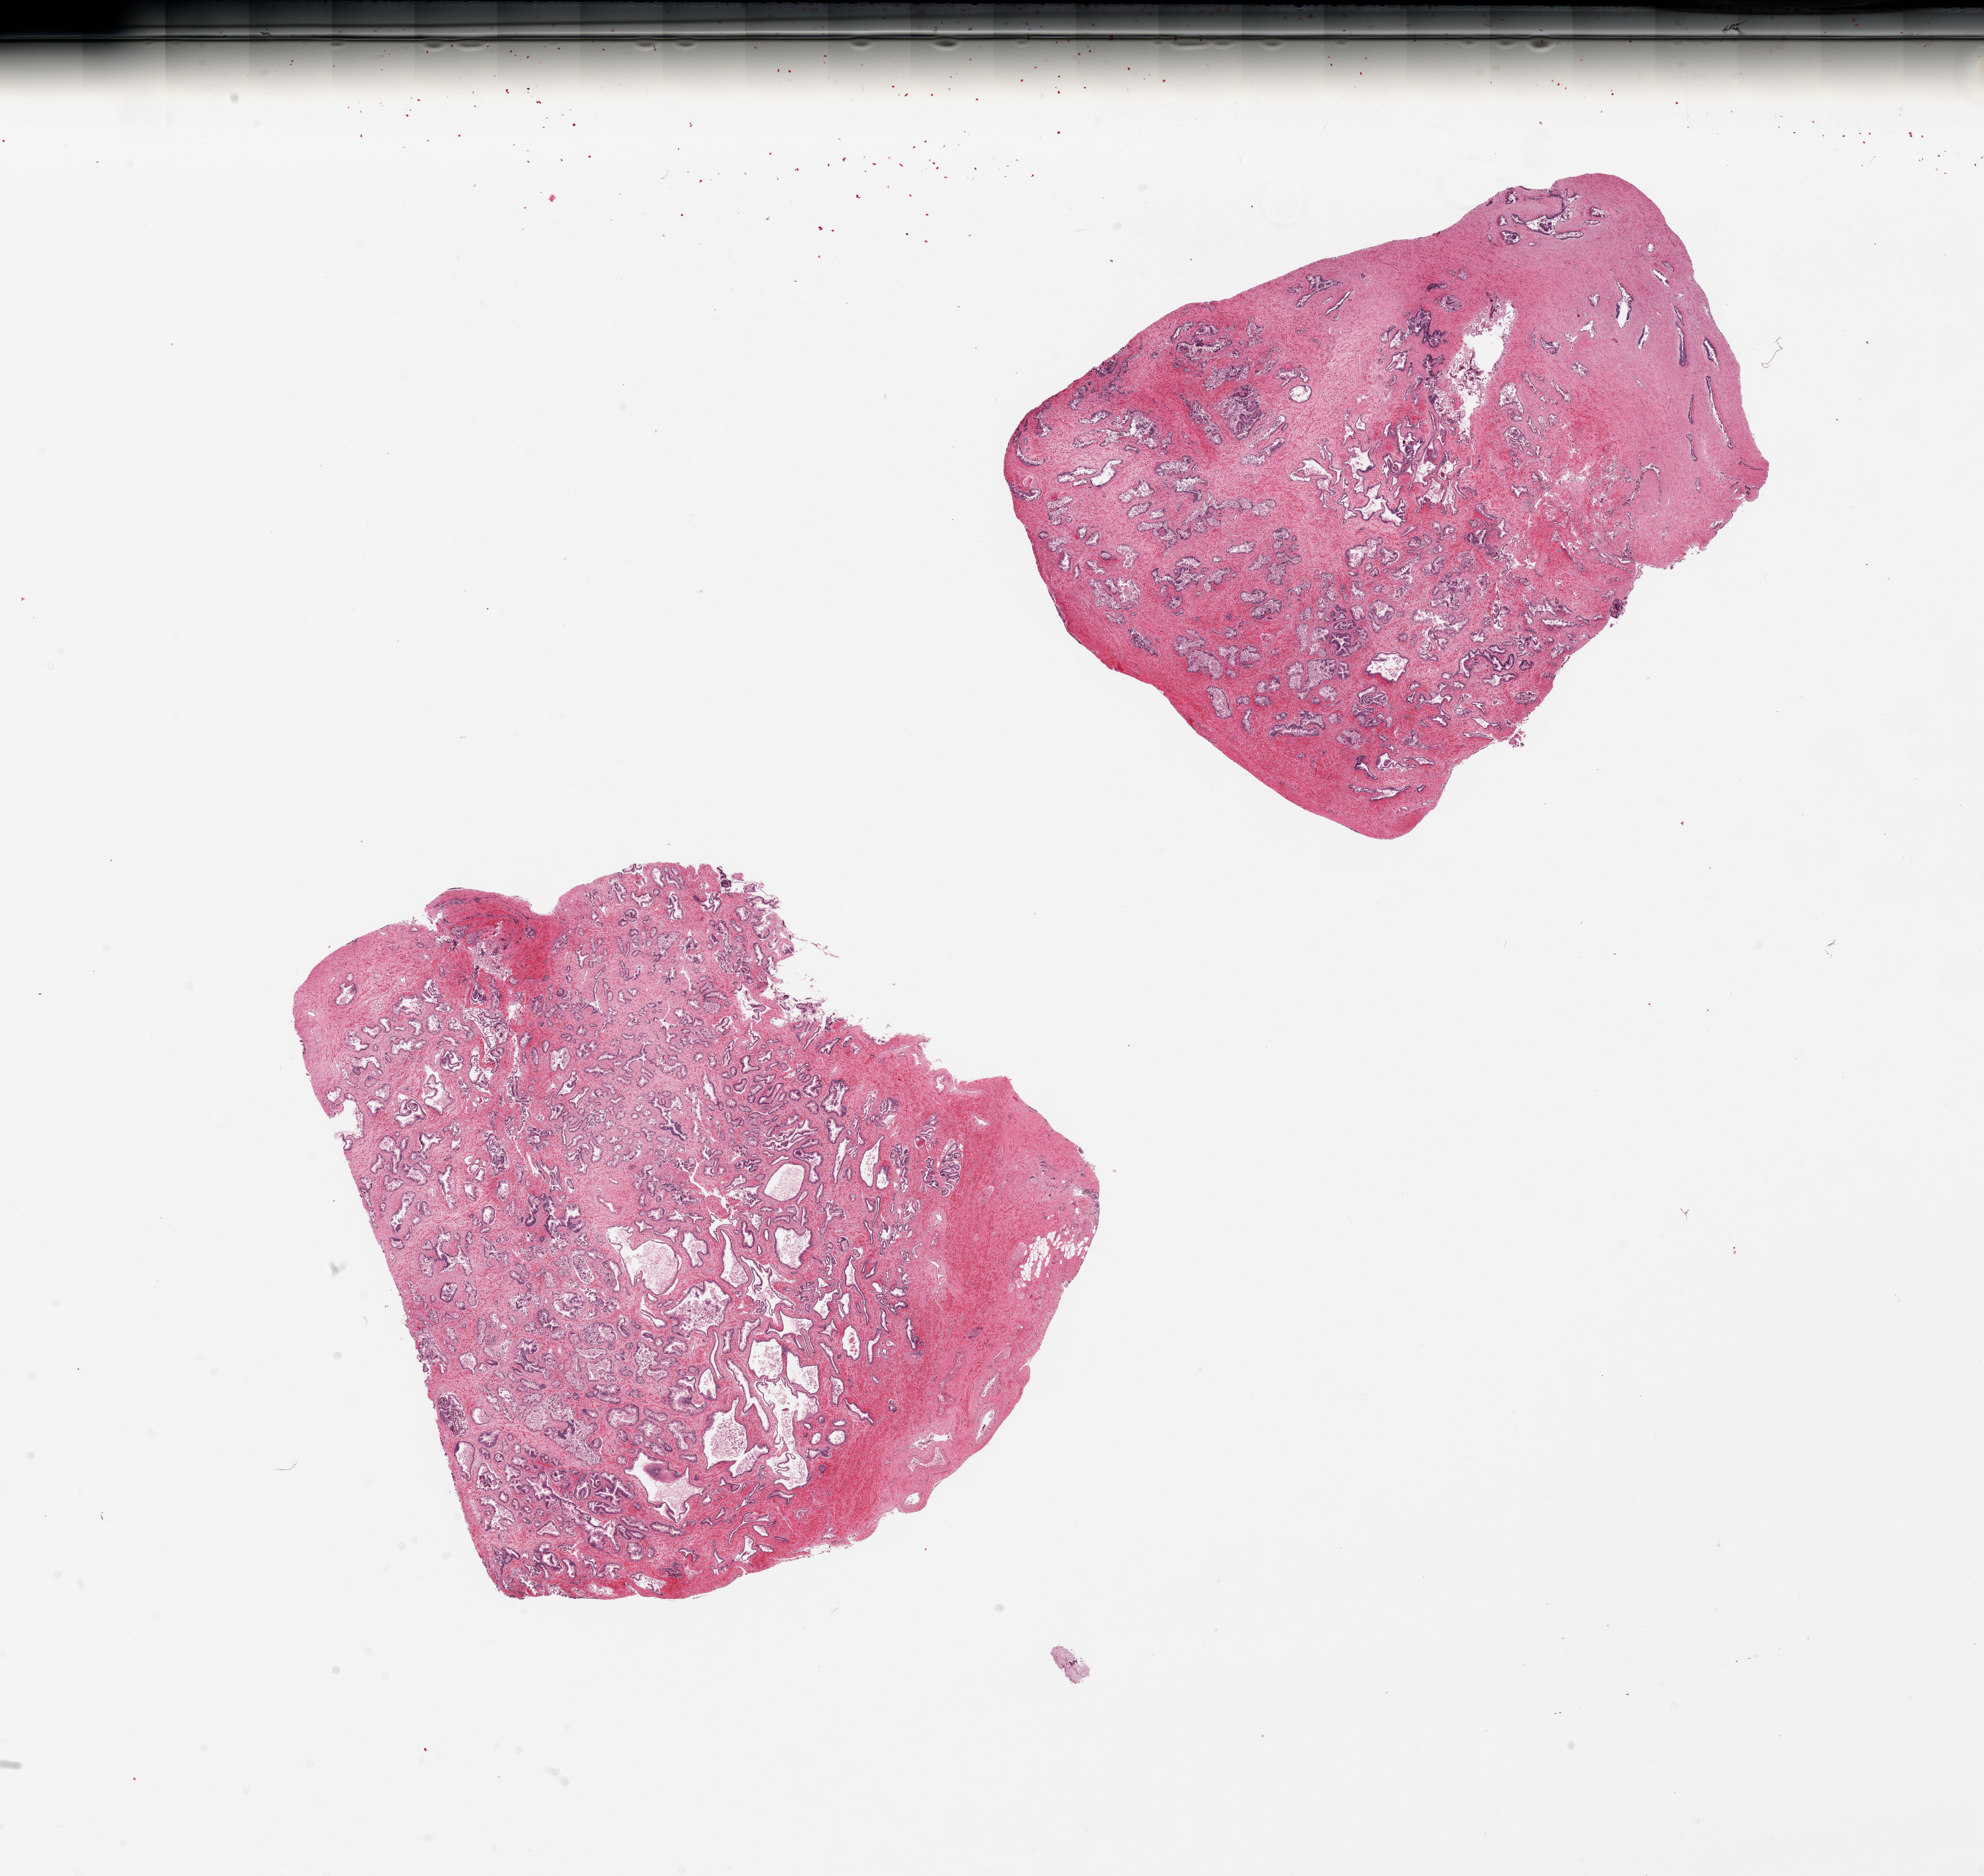
Digitized H&E-stained section, brightfield — low-resolution overview of the scanned area, about 23.6 x 22.3 mm (slide scanned at 20x). PAXgene-fixed, paraffin-embedded tissue. Sampled site (target tissue): prostate. Donor tissue sample.
* reviewer comment on this tissue sample: 2 pieces, glandular hyperplasia, glandular mucosa badly autolyzed; Adherent fibromuscular 'capsule'